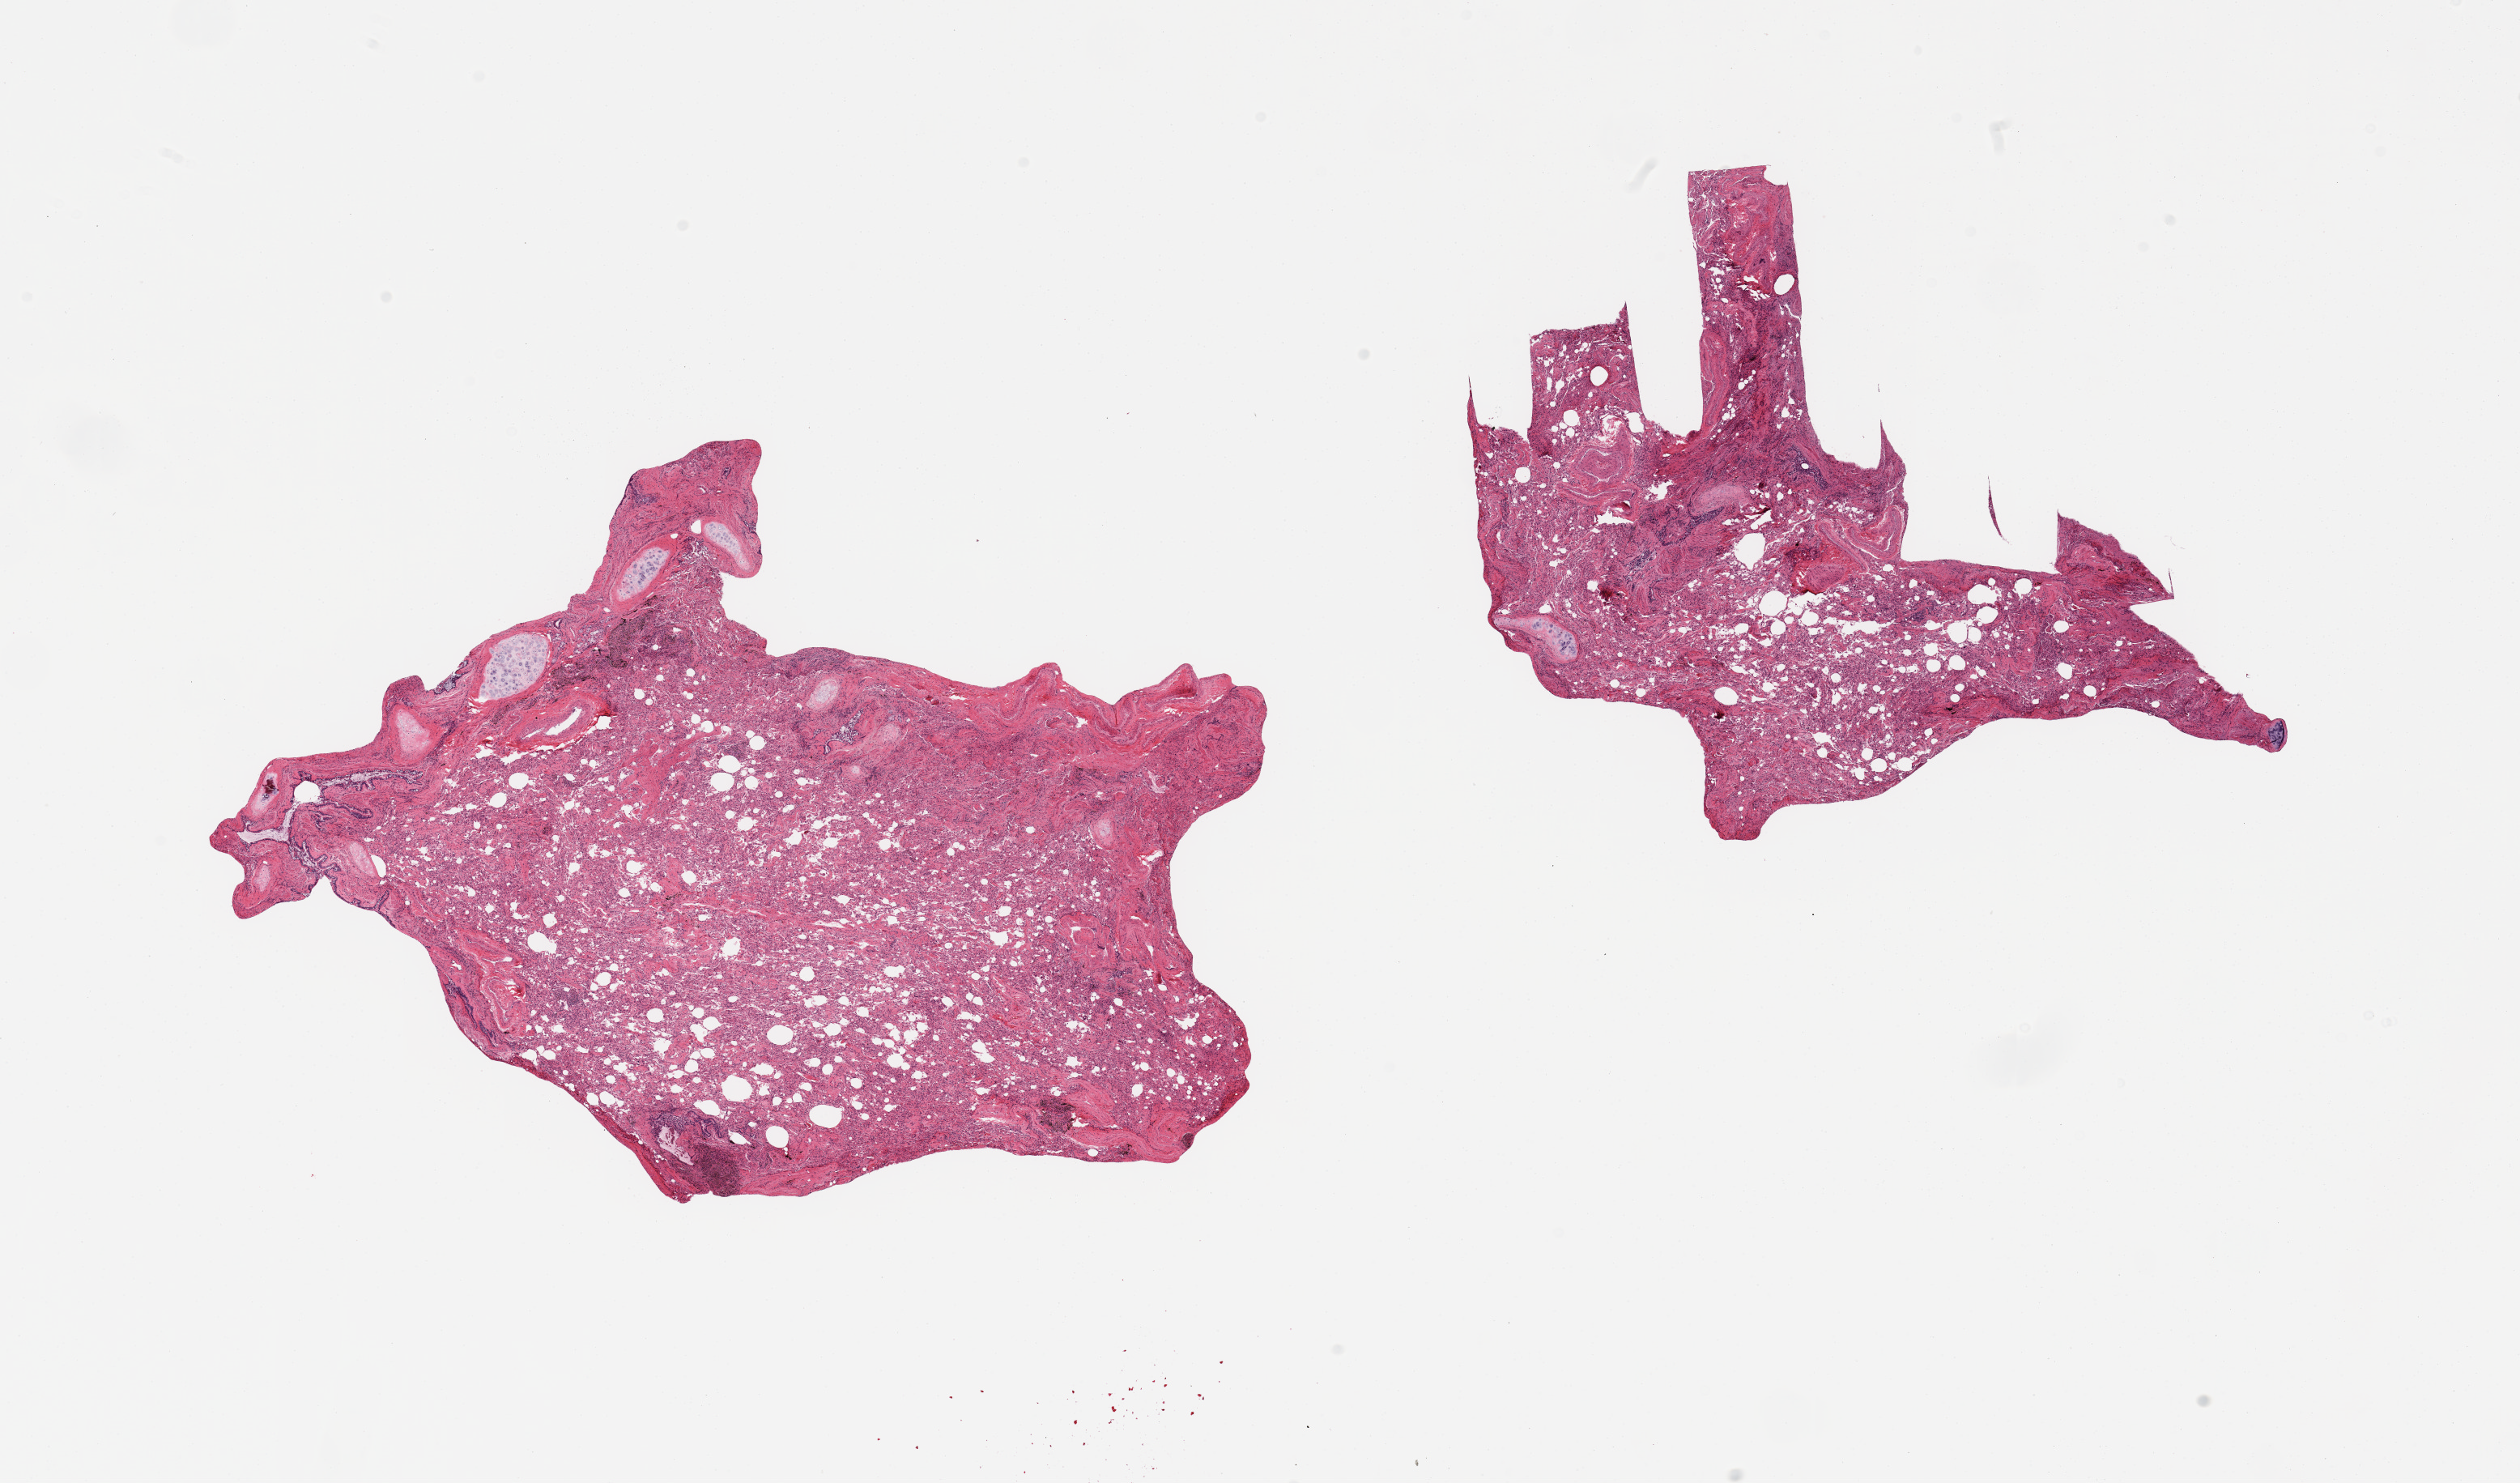
H&E whole-slide image, a low-resolution overview of the entire scanned area, about 24.6 x 14.5 mm (slide scanned at 20x). PAXgene-fixed, paraffin-embedded tissue. Sampled site (target tissue): lung. Donor tissue sample.
Pathologist's review note for this sample: 2 pieces; bronchi comprise 10% of each piece.